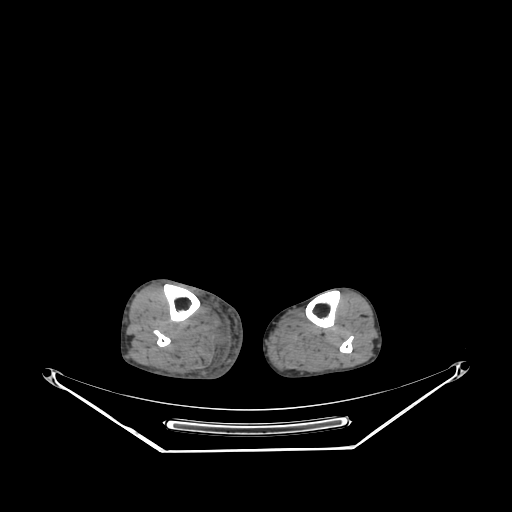
CT of an extremity soft-tissue mass (from a PET/CT study), one axial slice. Position 120 of 267 along the scan axis. 140 kVp. Soft-tissue window (W 400 / L 40 HU). 3.75 mm slice thickness. 512 × 512 image matrix, field of view 500 × 500 mm. Male patient. Case-level facts recorded for this patient, not image findings: histological type: pleiomorphic liposarcoma; grade: high; site of the primary tumour: right calf.
Outlined on this slice (expert contour drawn on MRI and transferred to this co-registered scan by the dataset authors):
- gross tumour volume including surrounding oedema: bounding box <212,336,220,344> (left, top, right, bottom; pixels)